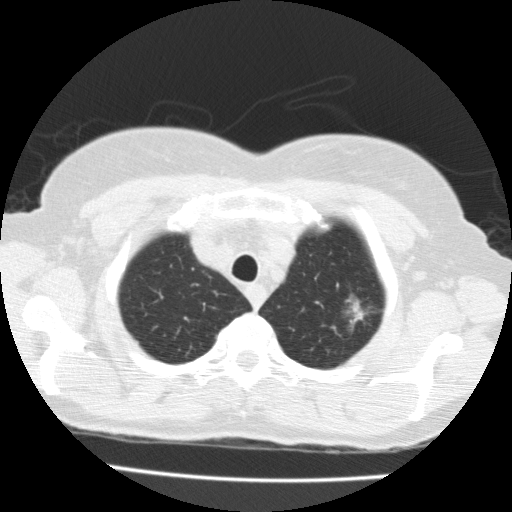
Low-dose screening chest CT, one axial slice. Slice 158 of 183 in the series (ordered by position). Lung window (W 1500 / L -600 HU). 2 mm slice thickness. 512 × 512 image matrix, field of view 320 × 320 mm.
Outlined on this slice (outlined manually by an expert reader):
- lesion 1 (tumor, upper lobe of left lung): bounding box <346,295,365,324> (left, top, right, bottom; pixels)